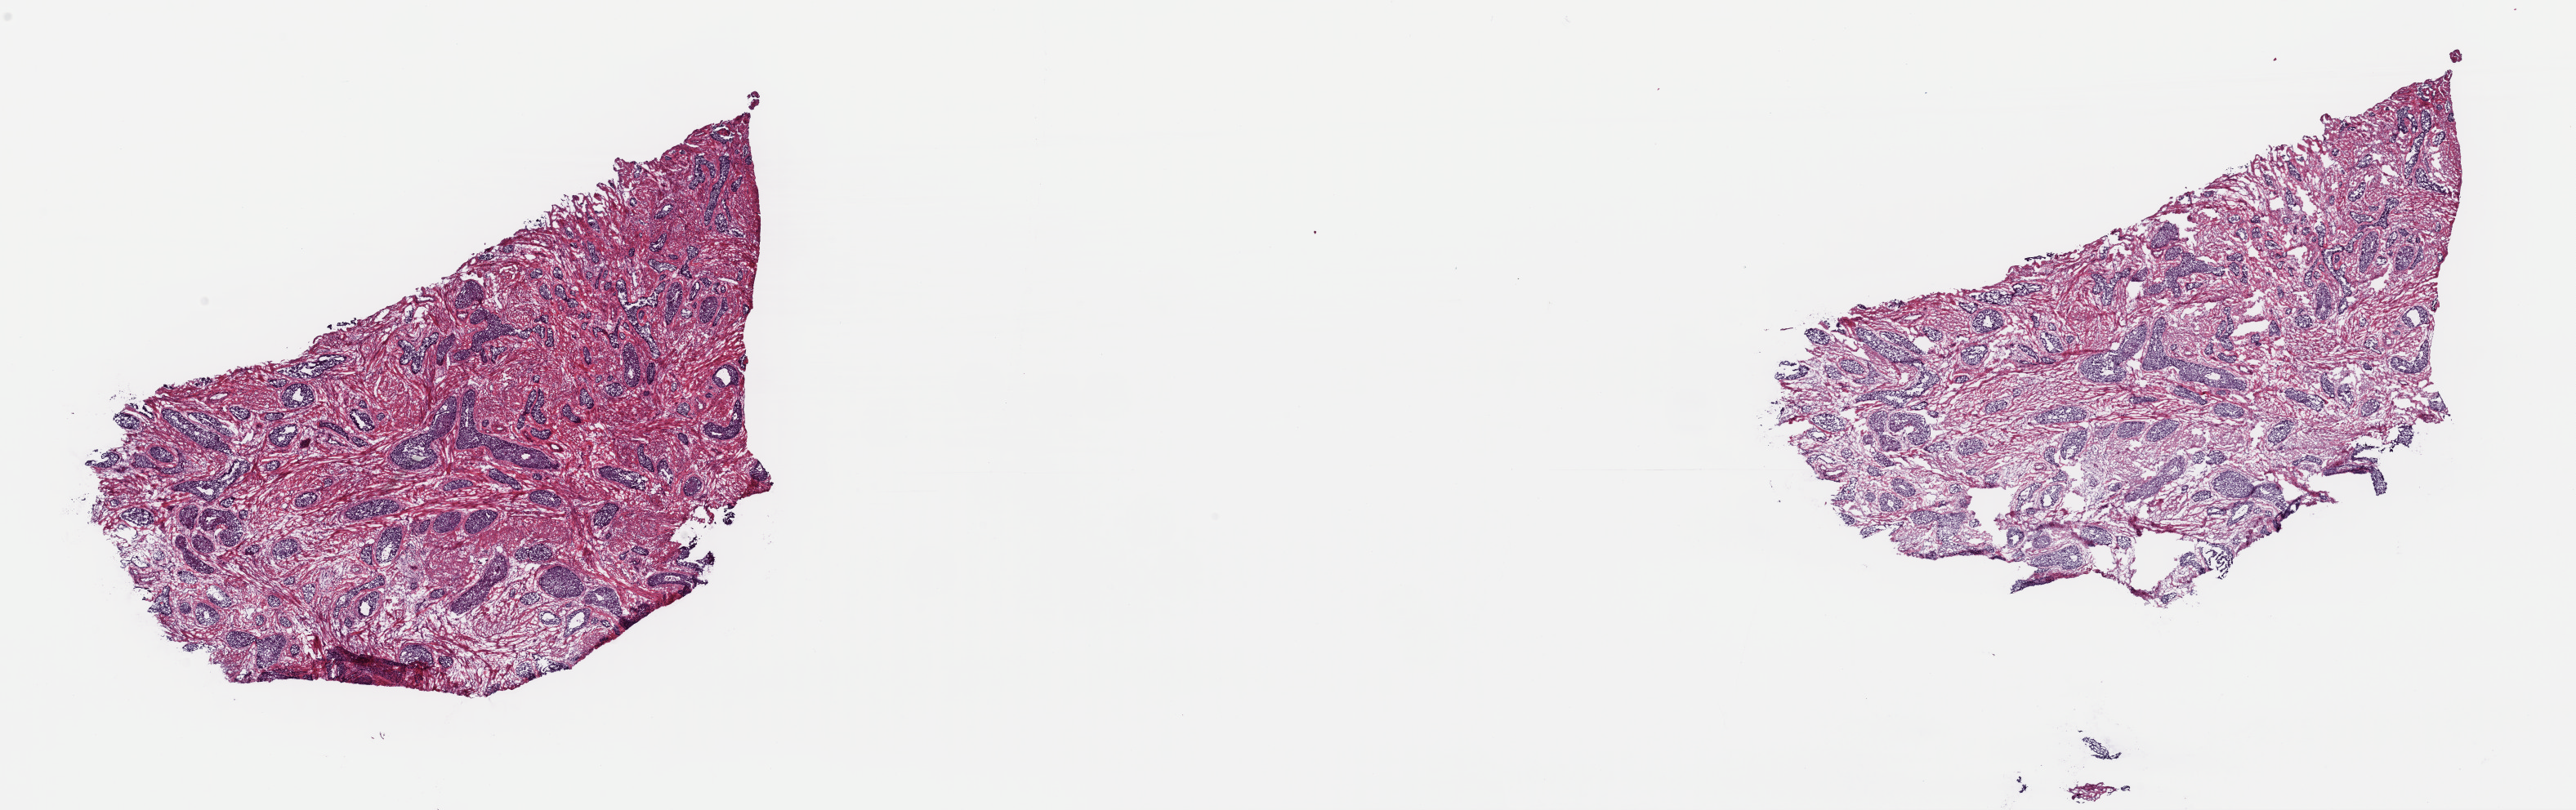
H&E whole-slide image, low-resolution overview of the scanned area, about 24.9 x 7.8 mm (slide scanned at 40x); frozen section from the top of the tissue portion; sample: primary tumour, cervix. Patient: female, age at initial diagnosis 37 years. Histologic grade: G3 (poorly differentiated). Slide review estimates, as recorded: tumour cells 60%, tumour nuclei 60%, normal cells 40%, stromal cells 0%, necrosis 0%. Inflammatory infiltration, as recorded: lymphocyte infiltration 5%, monocyte infiltration 0%, neutrophil infiltration 0%.
FIGO stage: IB1. Lymph nodes positive (case pathology): 0 of 20 examined. Diagnosis: Squamous cell carcinoma, NOS.